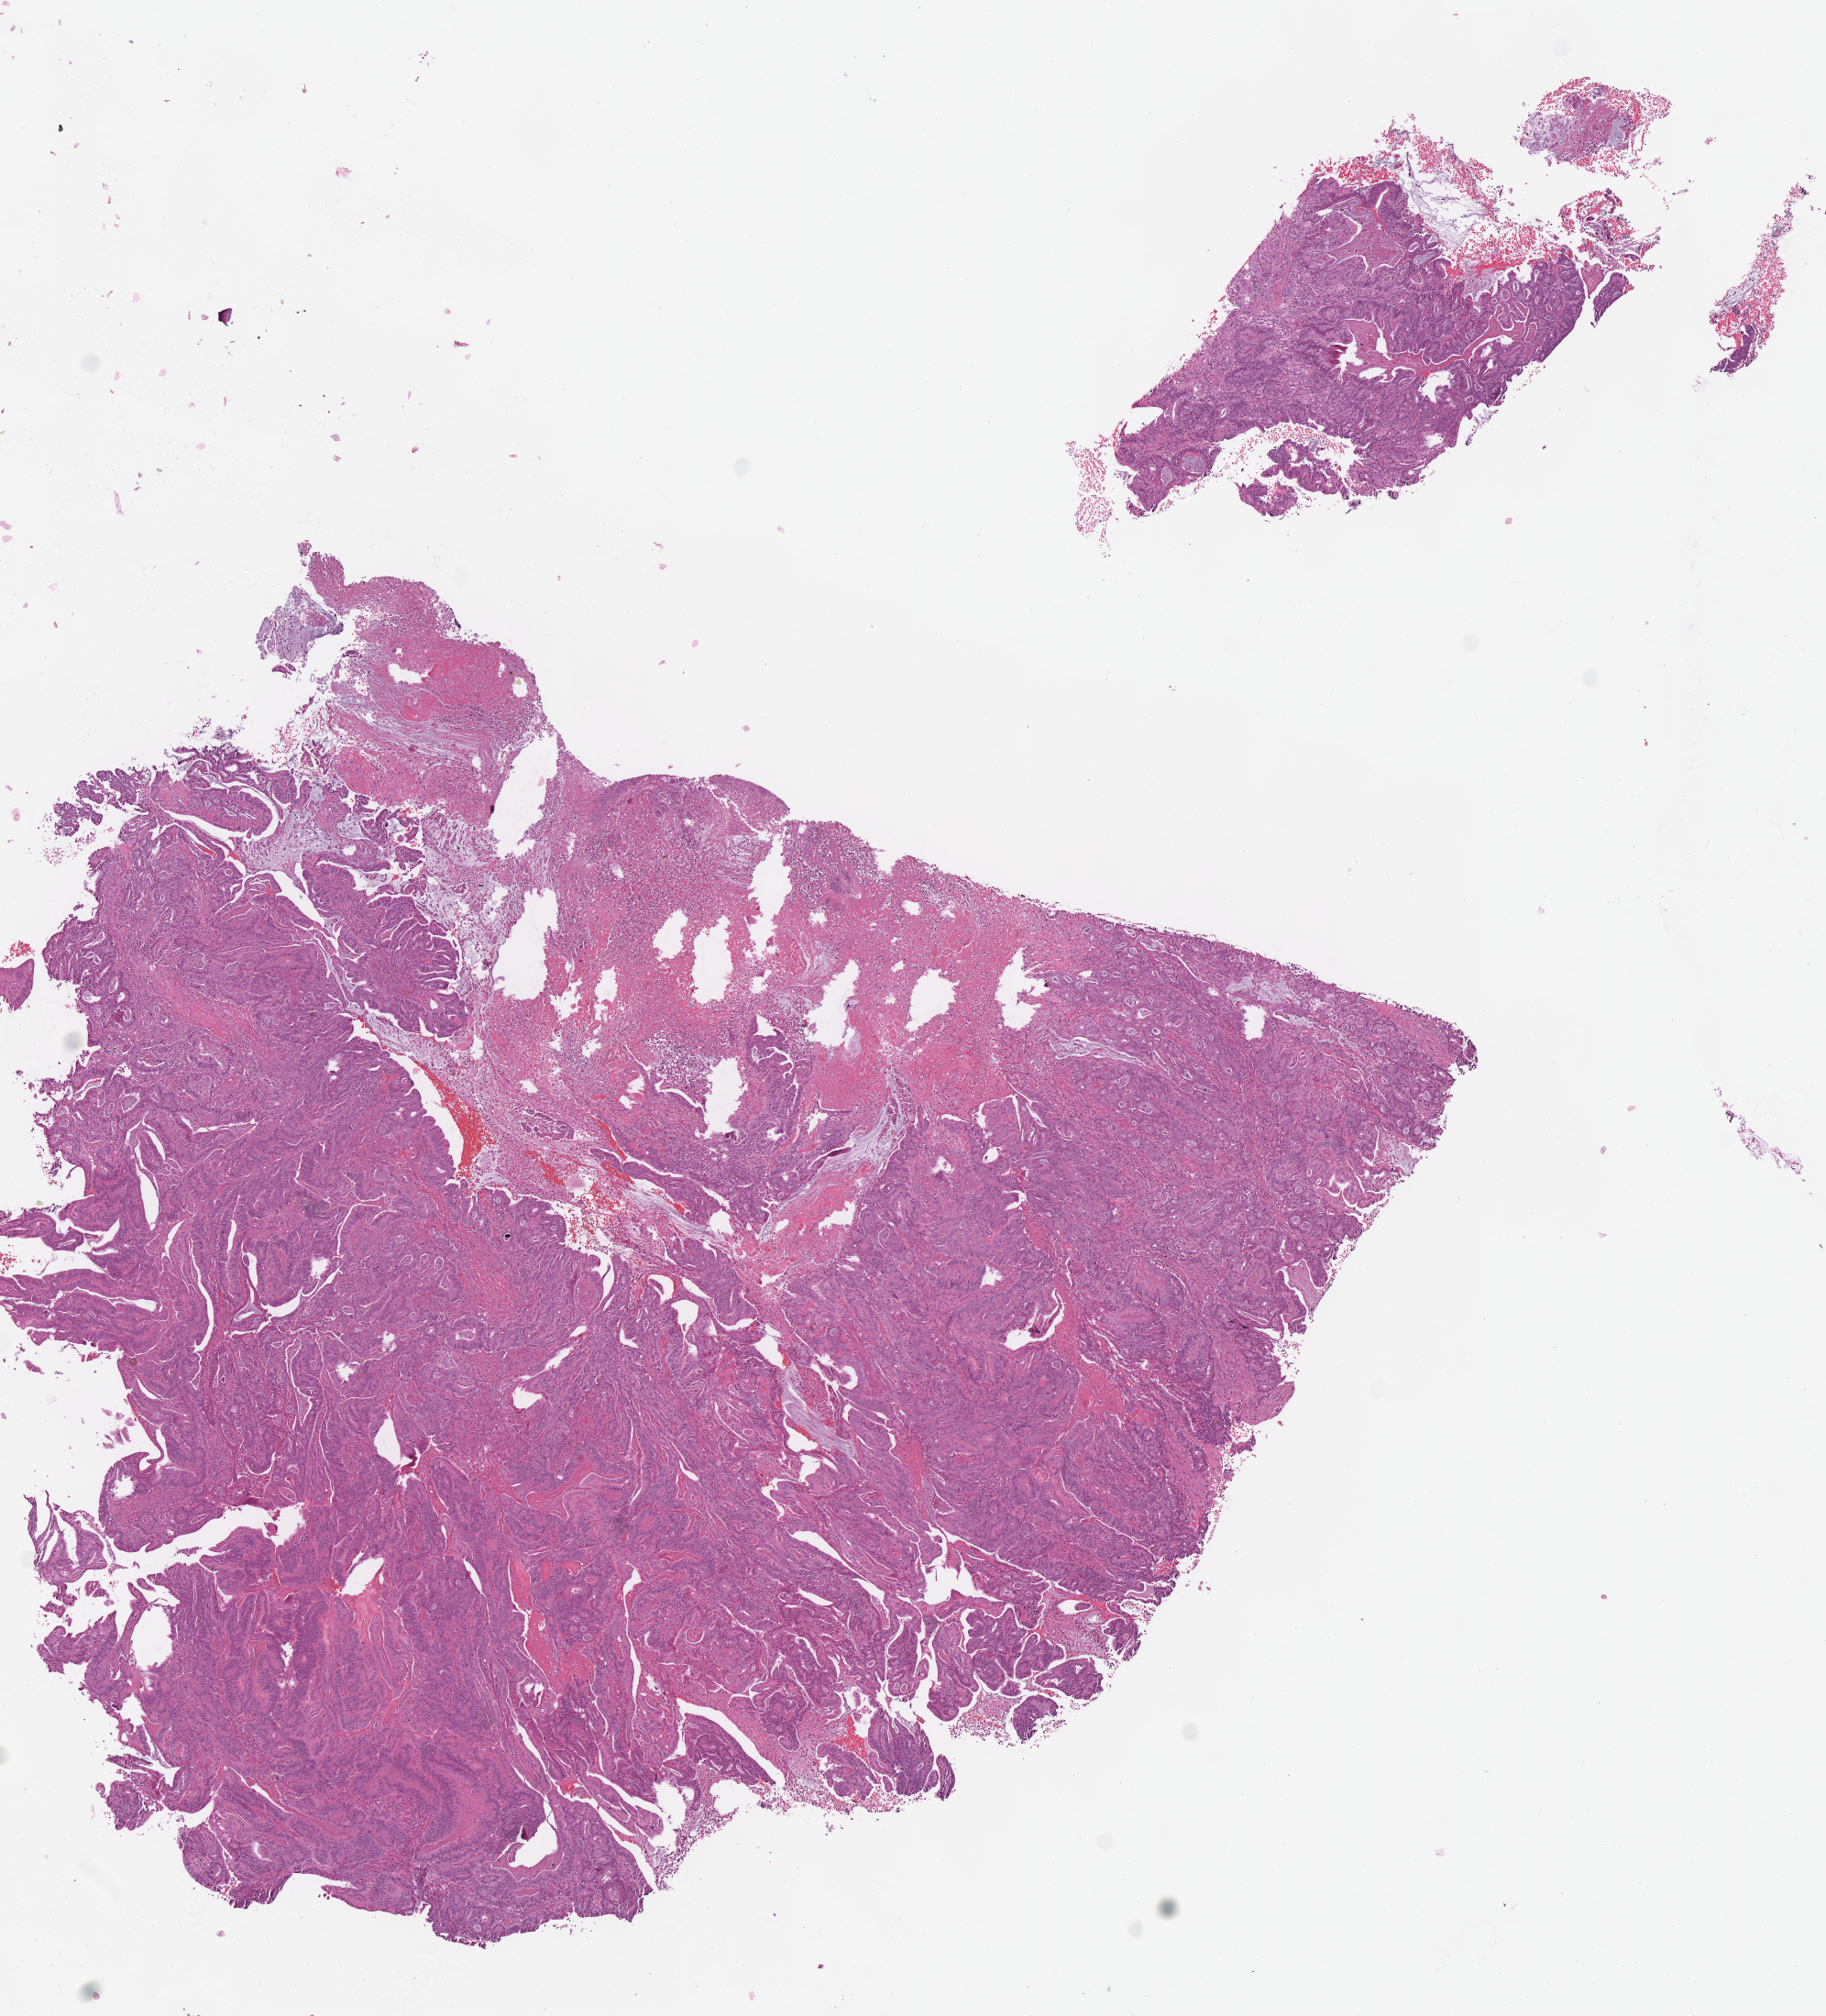
H&E-stained whole-slide image — low-resolution overview of the scanned area, about 7.8 x 8.6 mm (acquisition: 40x scan). Frozen section from the top of the tissue portion. Primary tumour sample from the colon. Female patient; age at initial diagnosis 82 years. Pathologist review of this section (percent, as recorded): tumour cells 80%, tumour nuclei 80%, normal cells 0%, stromal cells 15%, necrosis 5%.
• TNM: T3 N1 M0
• lymph nodes positive (case pathology): 1 of 29 examined
• AJCC pathologic stage: IIIB
• pathologic diagnosis: Adenocarcinoma, NOS (ascending colon)